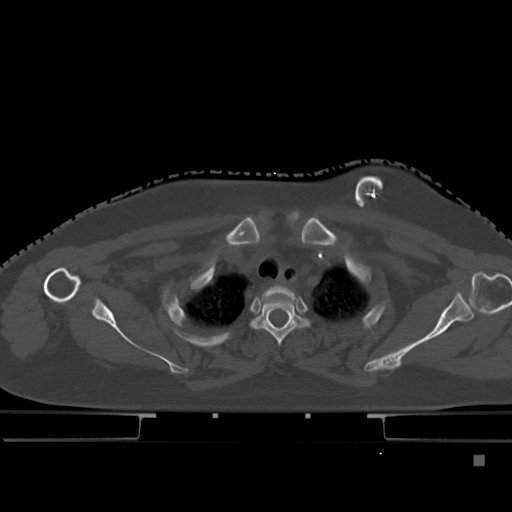
CT including the spine, one axial slice; slice 360 of 495 in the series (ordered by position); bone window (W 1800 / L 400 HU); 1.5 mm slice thickness; 512 × 512 image matrix. Female patient, age 33 years. From the clinical record (not read from this slice): primary cancer: breast.
Outlined on this slice (semi-automatic segmentation, software-assisted and operator-edited):
- T1 vertebra: box from (x=264, y=286) to (x=294, y=300) px
- T2 vertebra: (x=252, y=295)–(x=308, y=348)